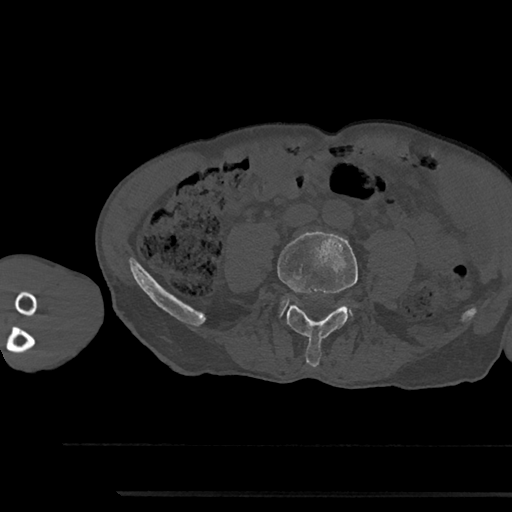
CT including the spine, one axial slice; slice 398 of 797 in the series (ordered by position); reconstruction kernel Br40s/3; 120 kVp; bone window (W 1800 / L 400 HU); 0.5 mm slice thickness; 512 × 512 image matrix. Male patient, age 79 years. From the clinical record (not read from this slice): primary cancer: prostate.
Annotated regions visible in this slice (semi-automatic segmentation, software-assisted and operator-edited):
- L4 vertebra: bounding box (x1, y1, x2, y2) in pixels: (277, 231, 358, 367)
- L5 vertebra: (280, 300, 287, 315)